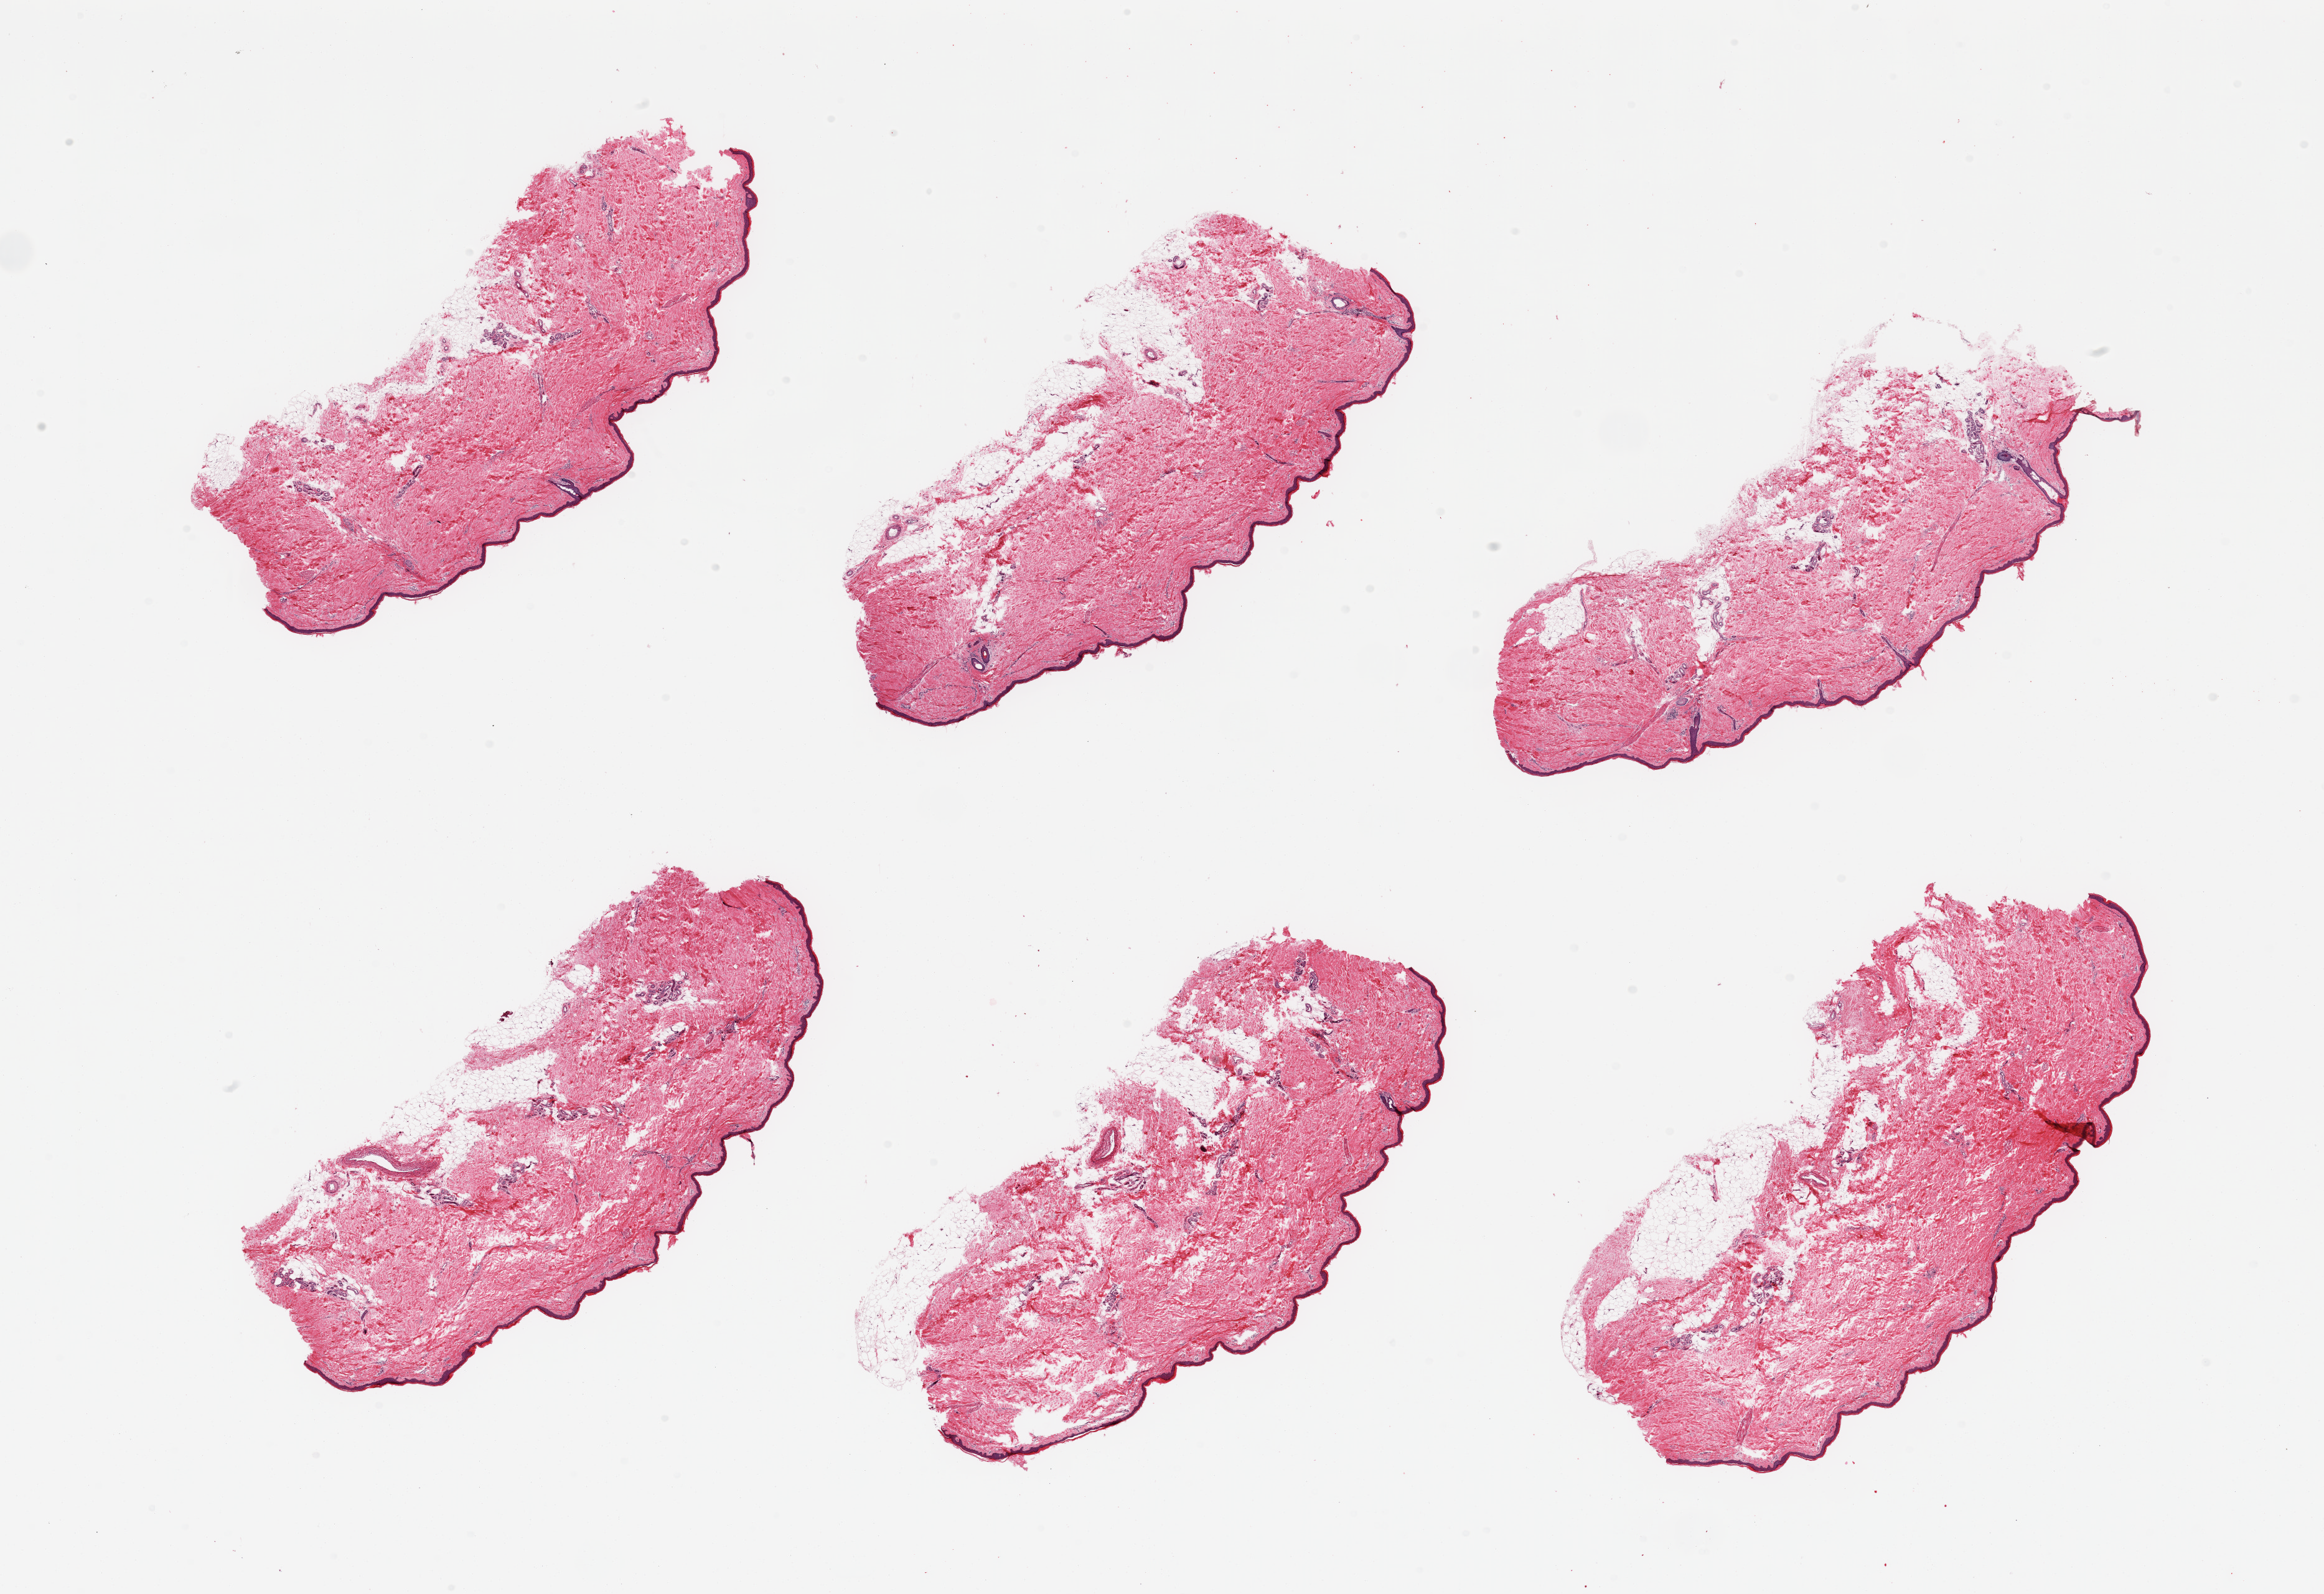
Whole-slide image, H&E stain, low-resolution overview of the scanned area, about 29.5 x 20.3 mm (from a 20x scan); PAXgene-fixed, paraffin-embedded tissue; target tissue: skin of lower leg; tissue donor sample.
Reviewer comment on this tissue sample: 6 pieces, trace adherent dermal fat nubbins up to ~1mm; squamous epithelium is ~40 microns.